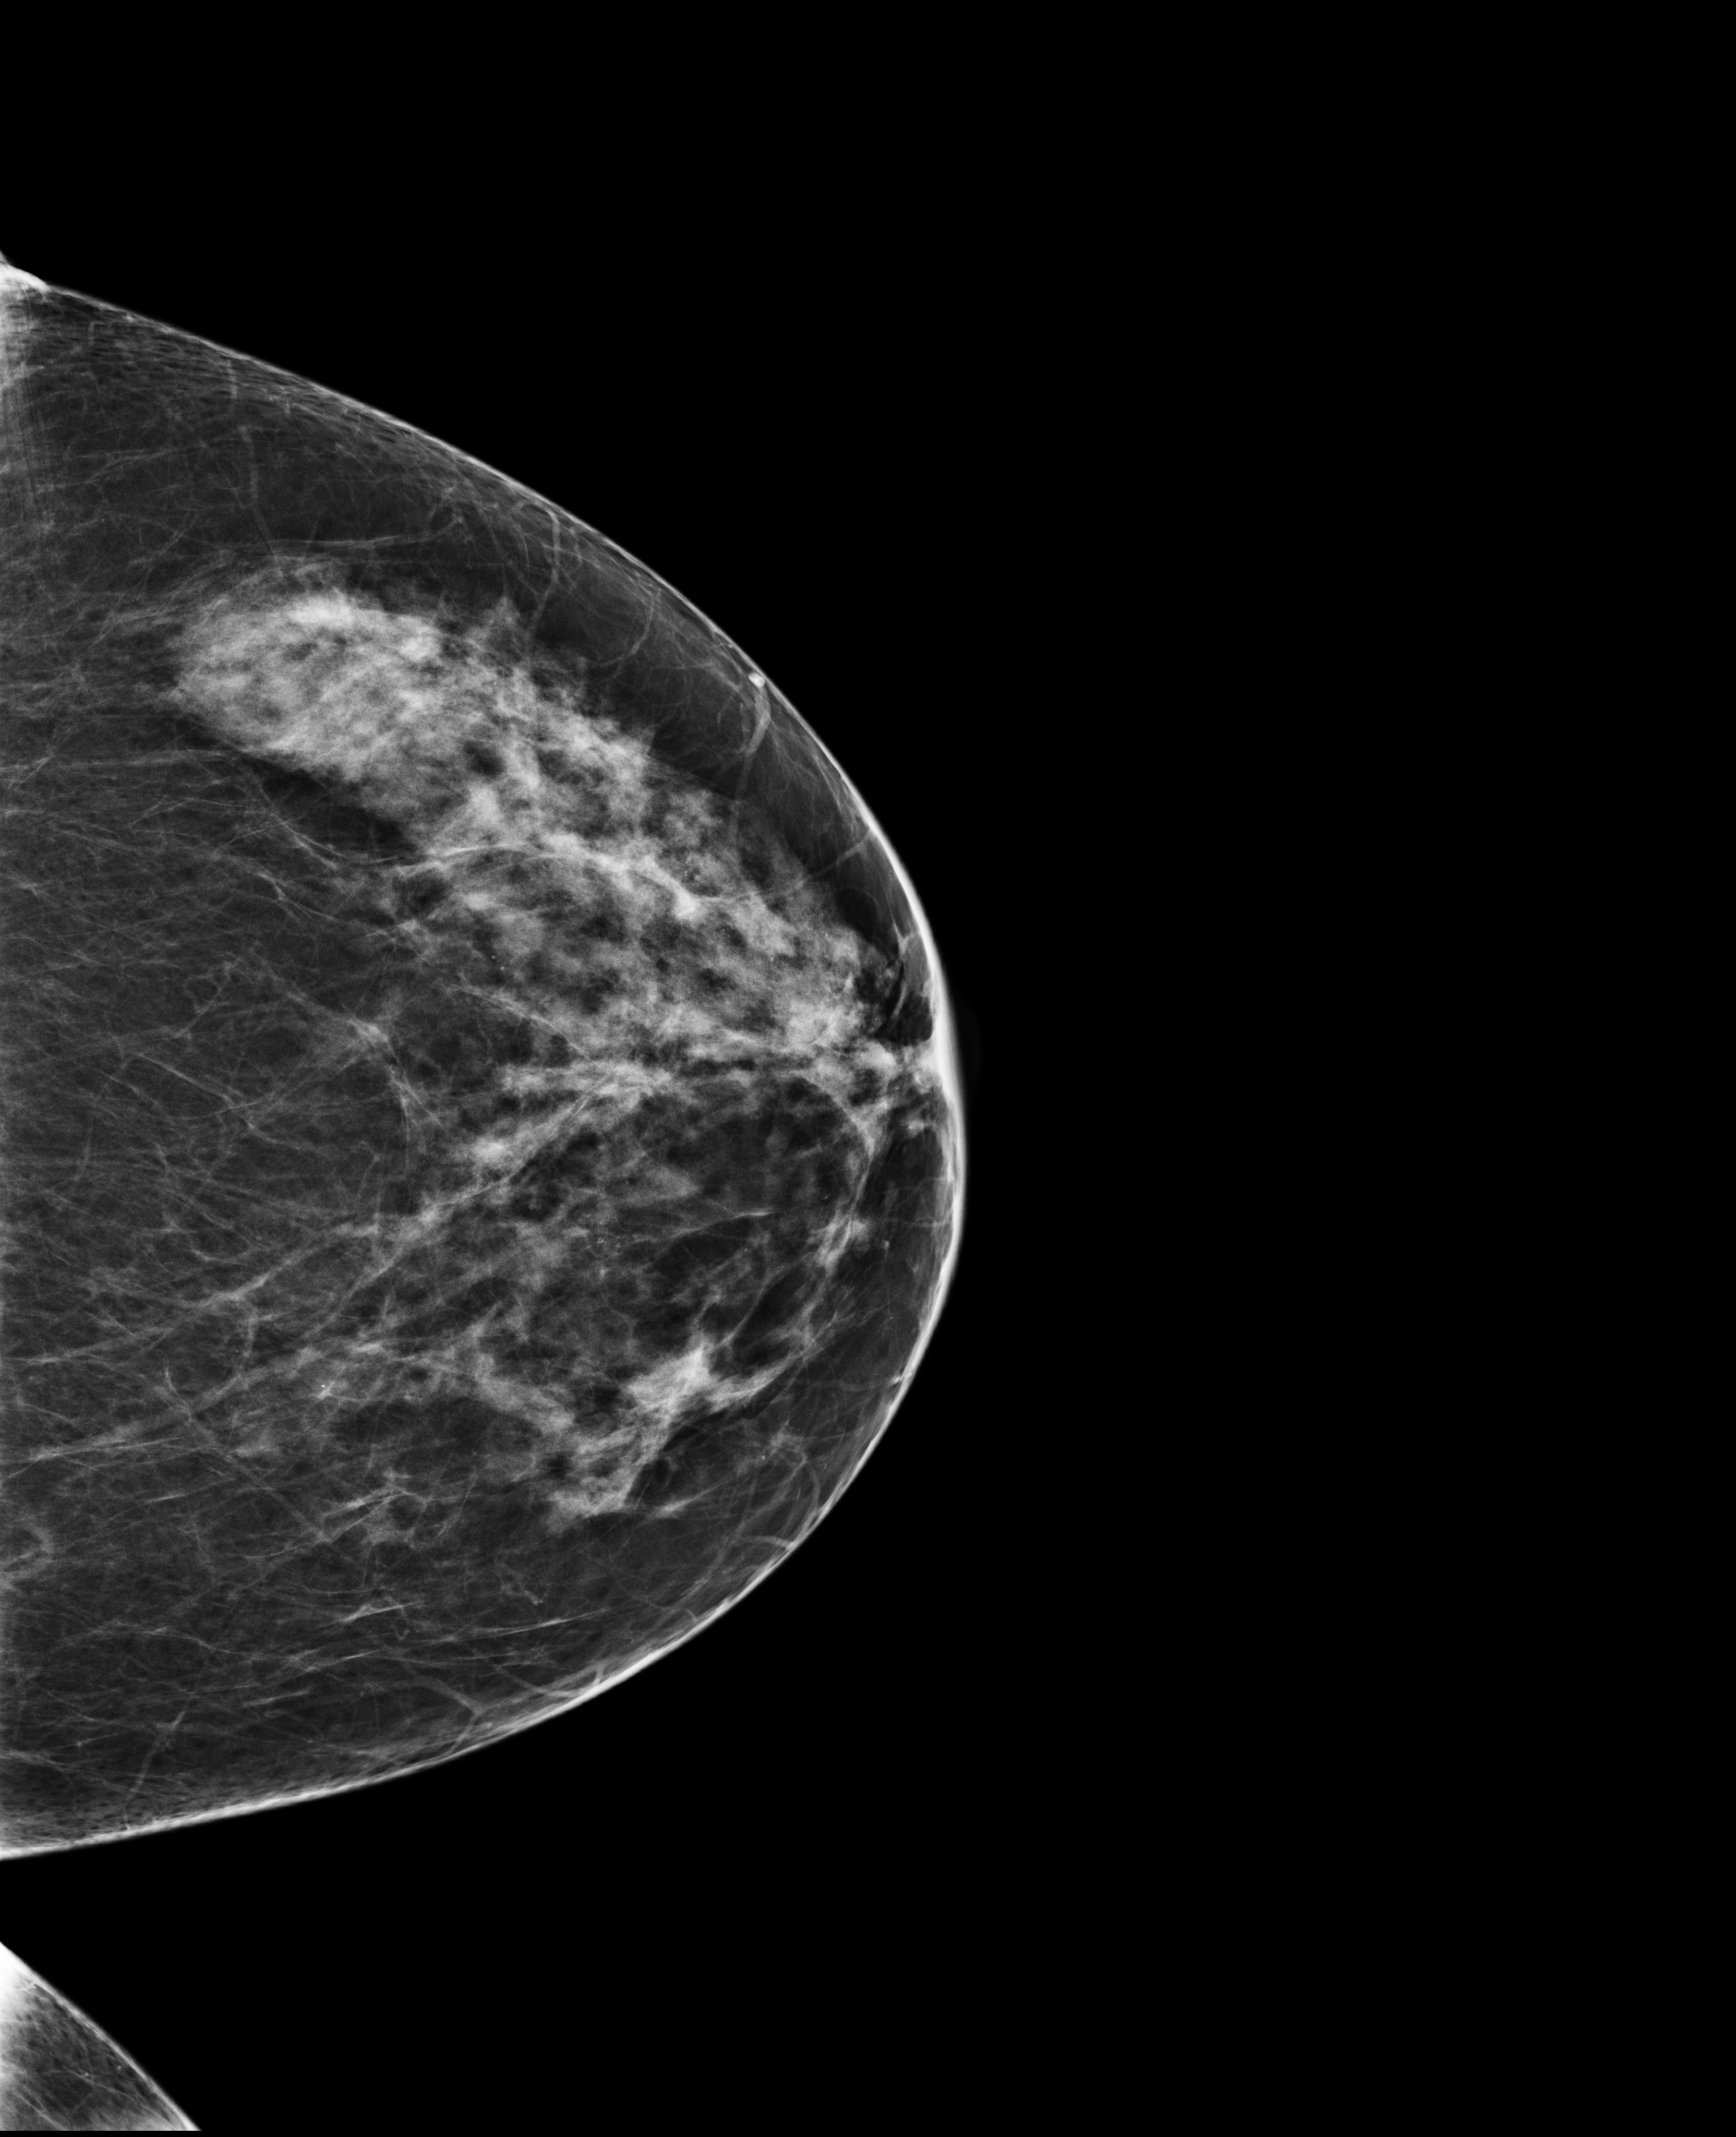
Screening examination.
Image type: full-field digital mammogram. Breast: left. Projection: CC view.